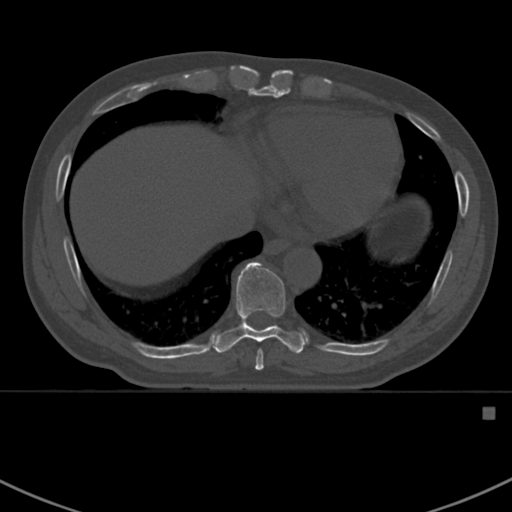
CT including the spine, one axial slice. Slice 384 of 412 in the series (ordered by position). Reconstruction kernel Br40s. Bone window (W 1800 / L 400 HU). 512 × 512 image matrix, field of view 358 × 358 mm. Male patient, age 59 years. From the clinical record (not read from this slice): primary cancer: prostate.
Outlined on this slice (semi-automatic segmentation, software-assisted and operator-edited):
- T8 vertebra: bounding box (x1, y1, x2, y2) in pixels: (255, 350, 264, 371)
- T9 vertebra: (213, 262, 306, 354)